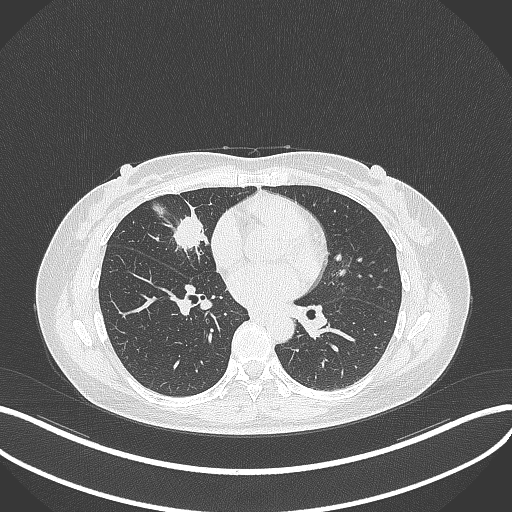
Chest CT, one axial slice. Slice 135 of 284 in the series (ordered by position). Lung window (W 1500 / L -600 HU). 1 mm slice thickness. 512 × 512 image matrix, field of view 400 × 400 mm. Patient: female, 43 years. From the clinical record (not read from this slice): clinical TNM (as recorded): T1c N3 M1; histopathological grade: G1.
Outlined on this slice (bounding box drawn by a radiologist):
- lung tumour (recorded histology: adenocarcinoma): bounding box (x1, y1, x2, y2) in pixels: (169, 214, 209, 252)